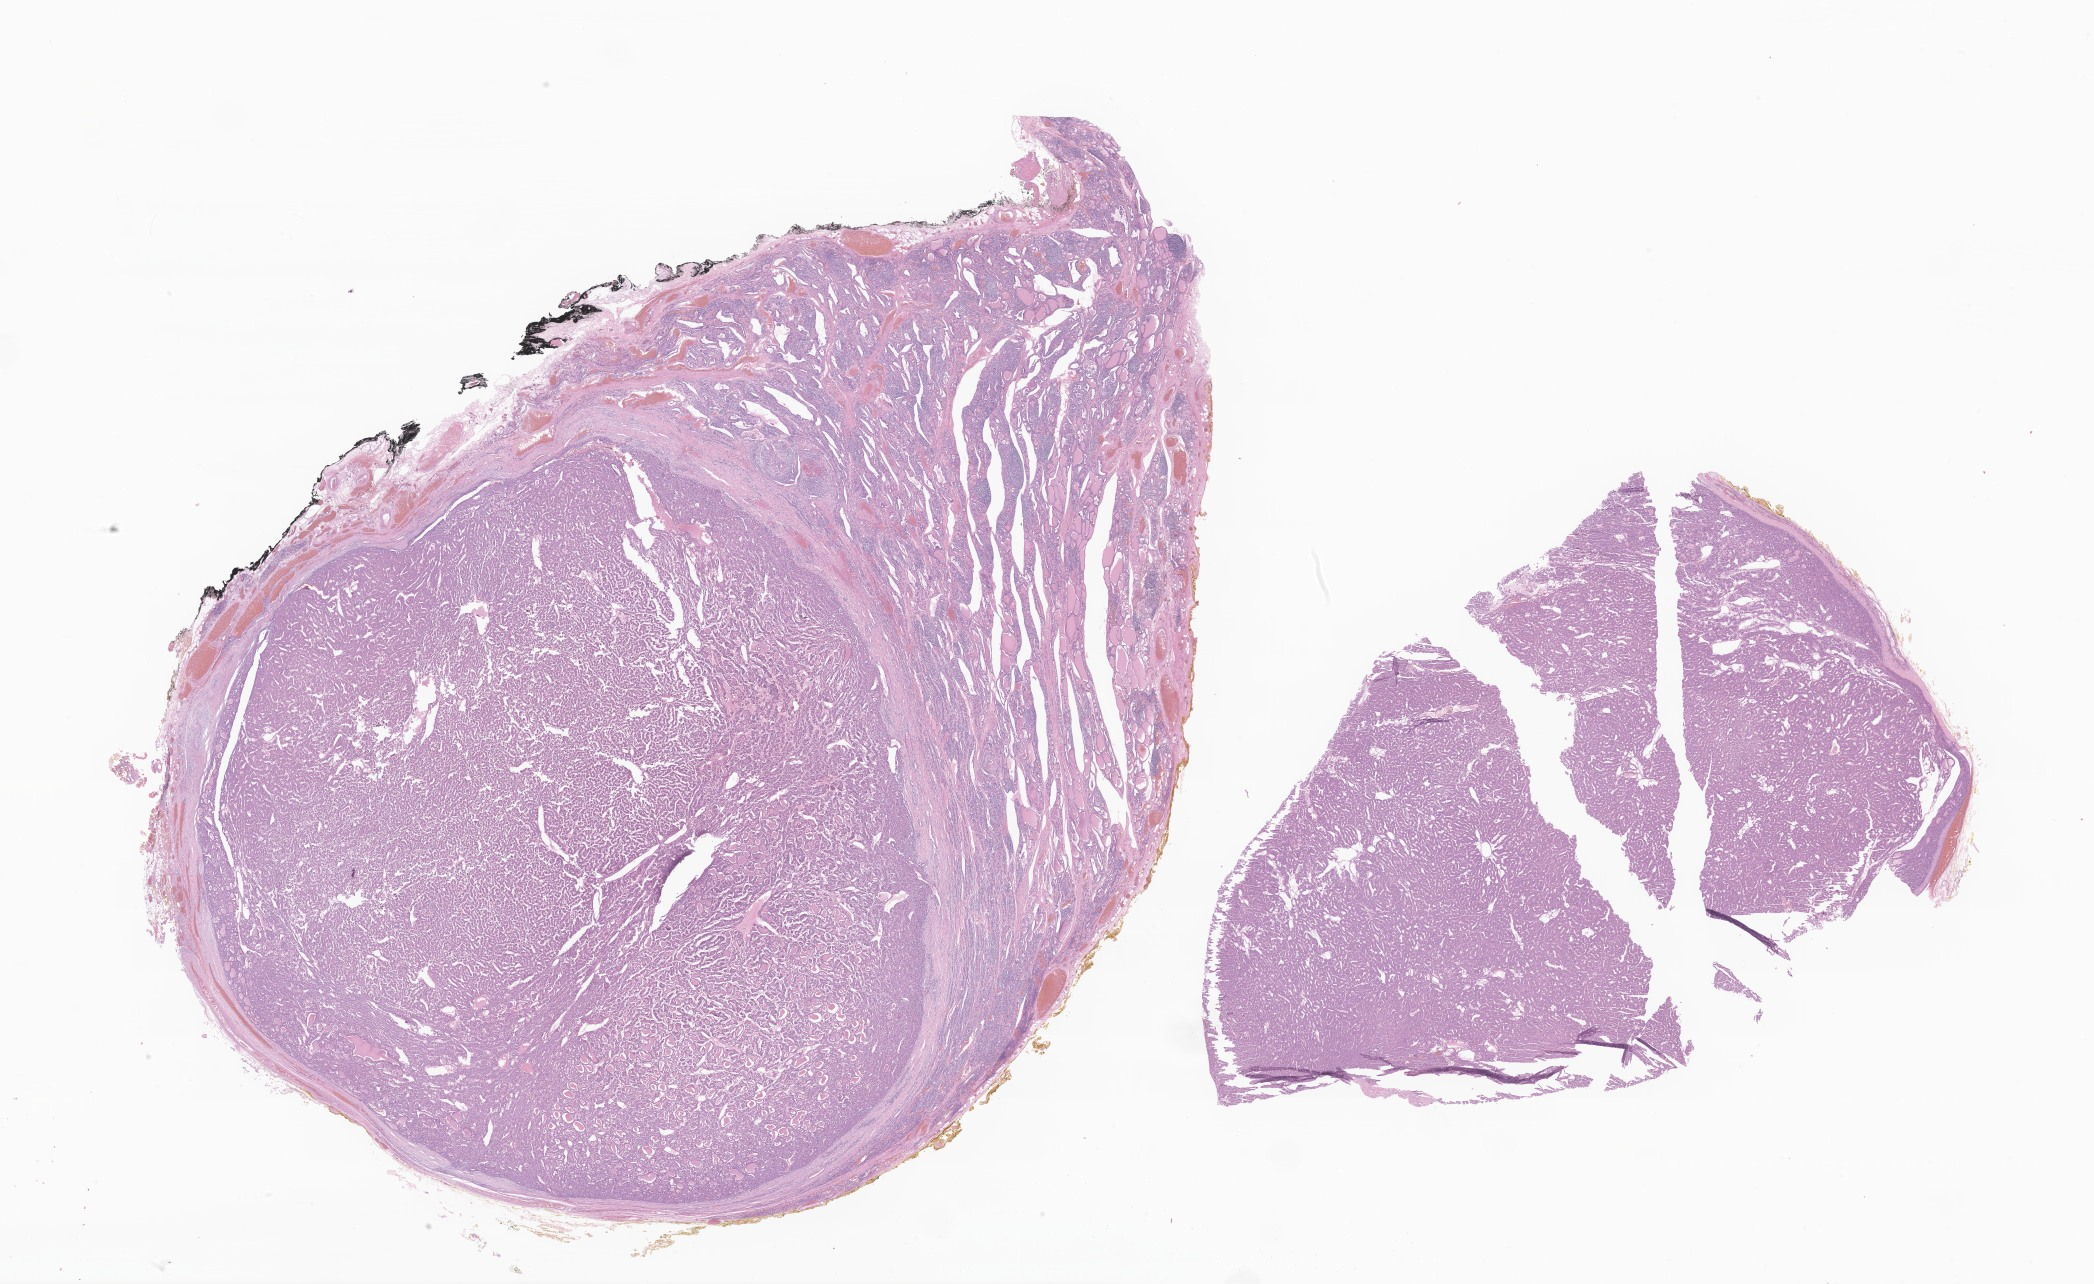
Haematoxylin and eosin whole-slide image of tumor tissue from the thyroid — low-resolution overview of the scanned area, about 35.3 x 21.6 mm; formalin-fixed, paraffin-embedded (FFPE) tissue. Female patient, age 185 months (15 years 5 months).
Diagnosis (ICD-O-3 morphology term): Carcinoma, NOS.